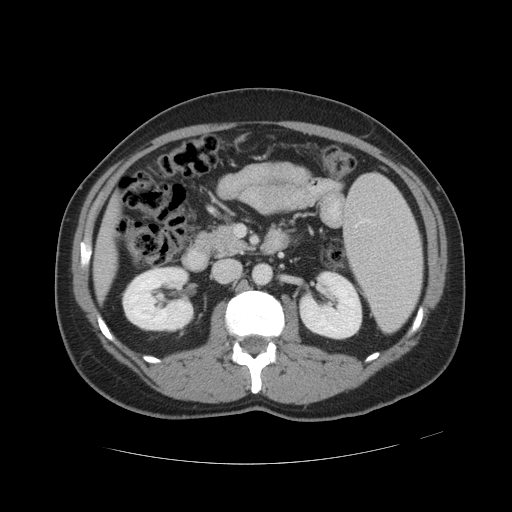
Contrast-enhanced abdominal CT, one axial slice; reconstruction kernel STANDARD; 120 kVp; intravenous contrast given; soft-tissue window (W 400 / L 40 HU); 5 mm slice thickness; 512 × 512 image matrix. Male patient, age 42 years. From the clinical record (not read from this slice): diagnosis: colorectal cancer liver metastases, imaged before liver resection; multiple liver metastases: yes; largest metastasis: 2.8 cm; chemotherapy before resection: yes.
Structures marked on this image (outlined manually by an expert reader):
- liver: box from (x=97, y=218) to (x=115, y=293) px
- planned liver remnant (the part of the liver to remain after resection): (x=97, y=237)–(x=115, y=293)